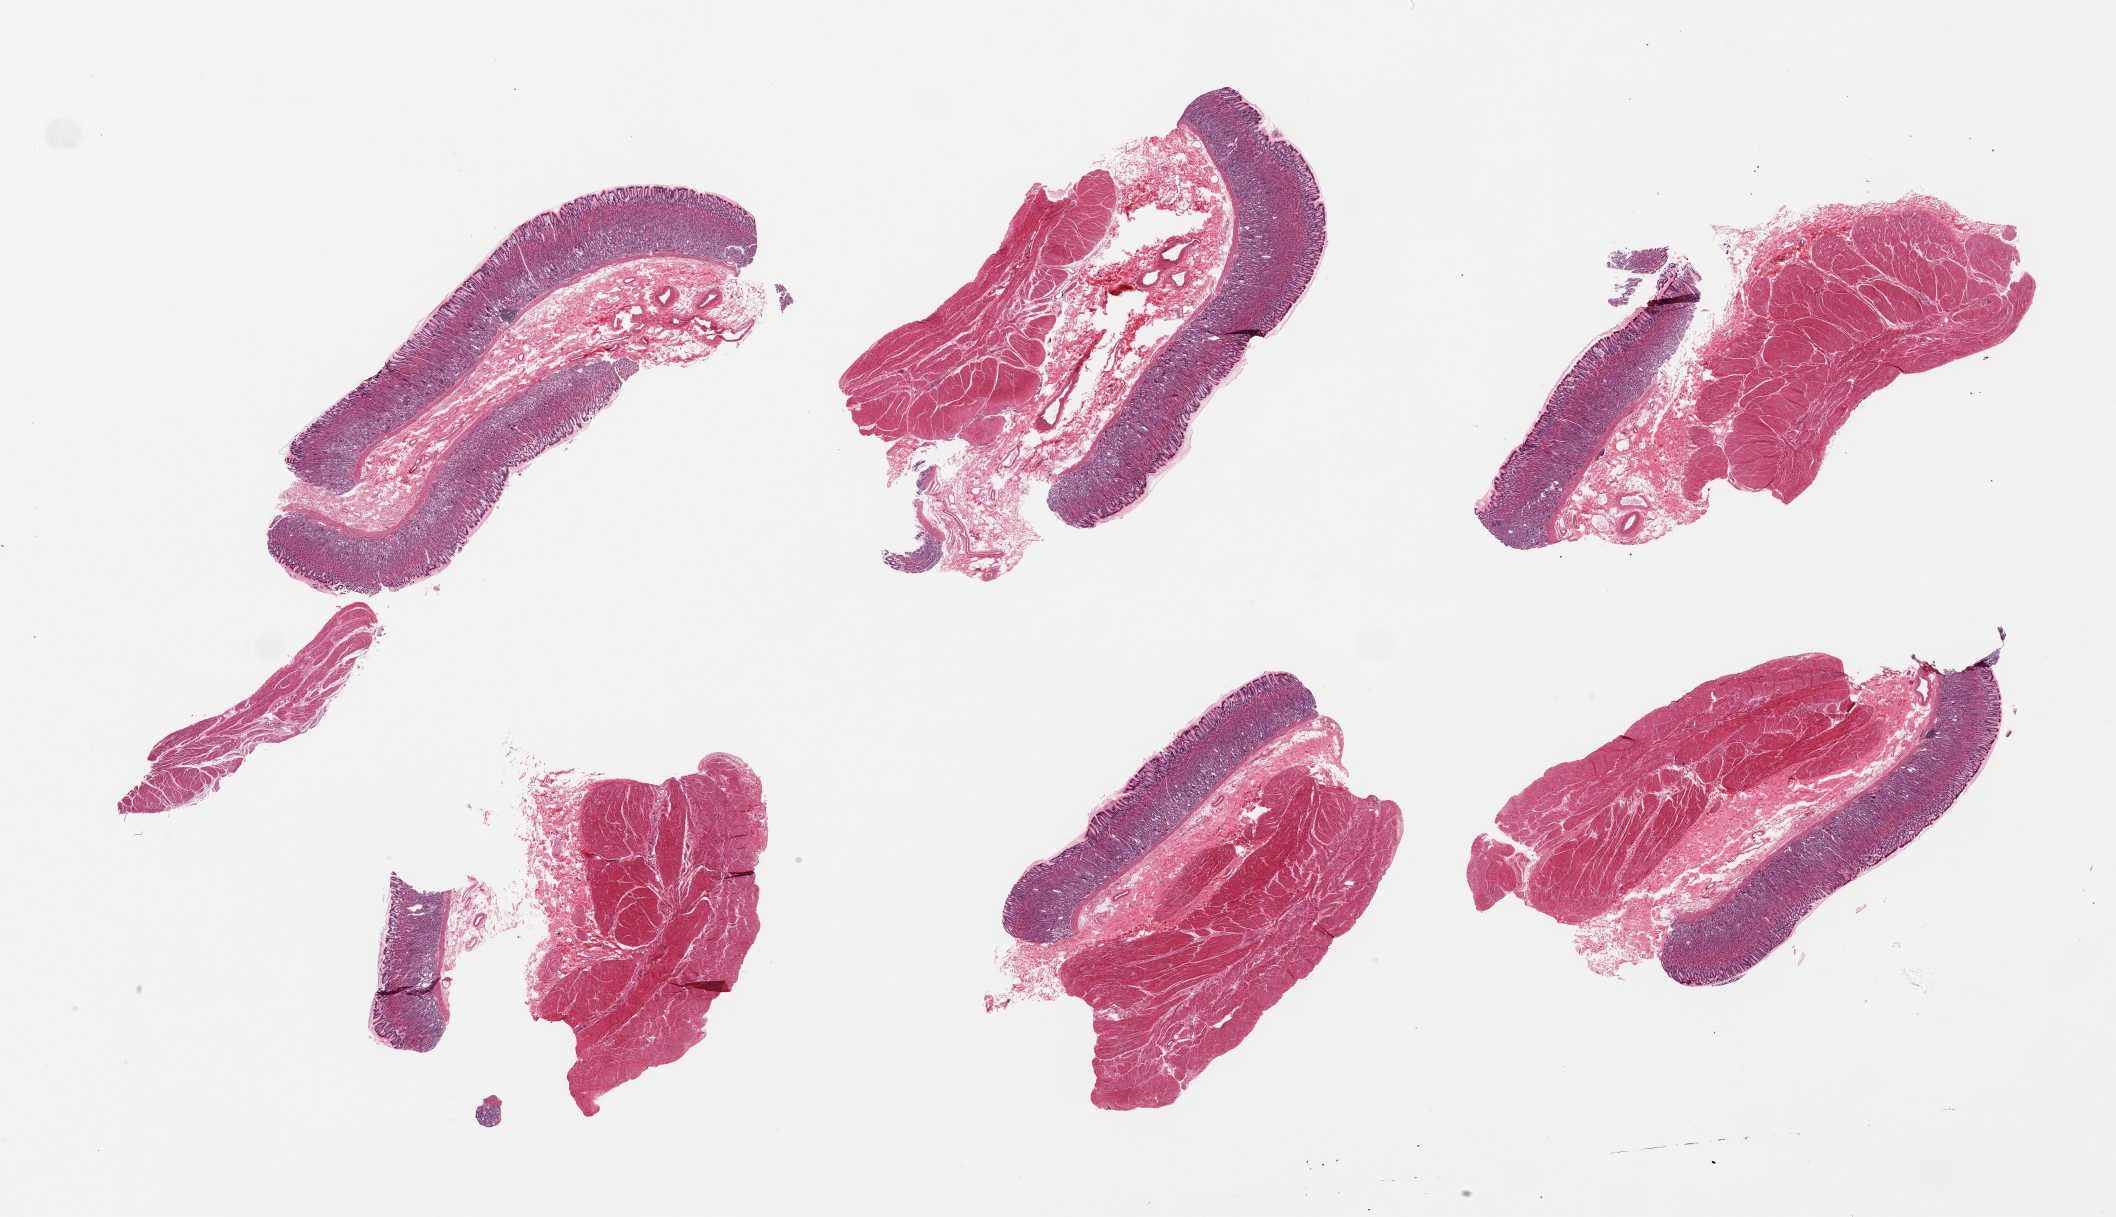
Digitized hematoxylin and eosin (H&E)-stained section, brightfield, whole scanned area (about 33.5 x 19.3 mm) shown as a low-resolution overview. PAXgene-fixed paraffin-embedded (PFPE) section. Target tissue: stomach. Tissue donor sample. Donor sex: male.
Reviewer comment on this tissue sample: 6 pieces, mucosa well preserved, ~1mm, ~20-30% thickness.